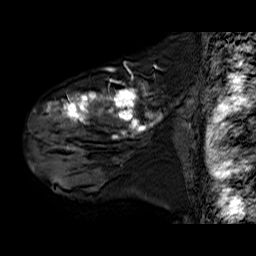
Breast MRI (dynamic contrast-enhanced), one sagittal slice; slice 46 of 60 in the series (ordered by position); dynamic contrast-enhanced series, time point 2 of 6 at this slice position (early post-contrast); 1.5 T; TE 6.3 ms, TR 32.9 ms; 4 mm slice thickness; 256 × 256 image matrix, field of view 200 × 200 mm. Female patient. Case-level facts recorded for this patient, not image findings: setting: breast cancer imaged before/during neoadjuvant chemotherapy; receptor status: HER2-positive.
Outlined on this slice (semi-automatically segmented with operator editing):
- analysis volume of interest (the breast-tissue region the enhancement analysis was run in; not a lesion): box from (x=30, y=79) to (x=182, y=180) px
- tumour enhancement mask (voxels above the 100 % enhancement threshold inside the analysis volume of interest): (x=47, y=84)–(x=163, y=148)